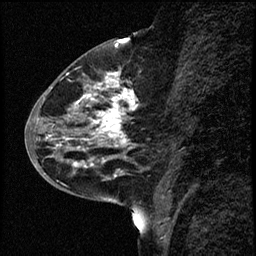
Breast MRI (dynamic contrast-enhanced), one sagittal slice; slice 26 of 68 in the series (ordered by position); dynamic contrast-enhanced study with each time point stored as its own series, time point 2 of 3 at this slice position (early post-contrast, ordered by acquisition time); 1.5 T; TE 4.2 ms, TR 17.6 ms; 2 mm slice thickness; 256 × 256 image matrix, field of view 200 × 200 mm. Female patient, age 52 years. From the clinical record (not read from this slice): setting: breast cancer imaged before/during neoadjuvant chemotherapy; receptor status: HER2-positive.
Outlined on this slice (semi-automatically segmented with operator editing):
- analysis volume of interest (the breast-tissue region the enhancement analysis was run in; not a lesion): bounding box [x1, y1, x2, y2] px = [50, 61, 149, 184]
- tumour enhancement mask (voxels above the 100 % enhancement threshold inside the analysis volume of interest): [53, 73, 135, 168]